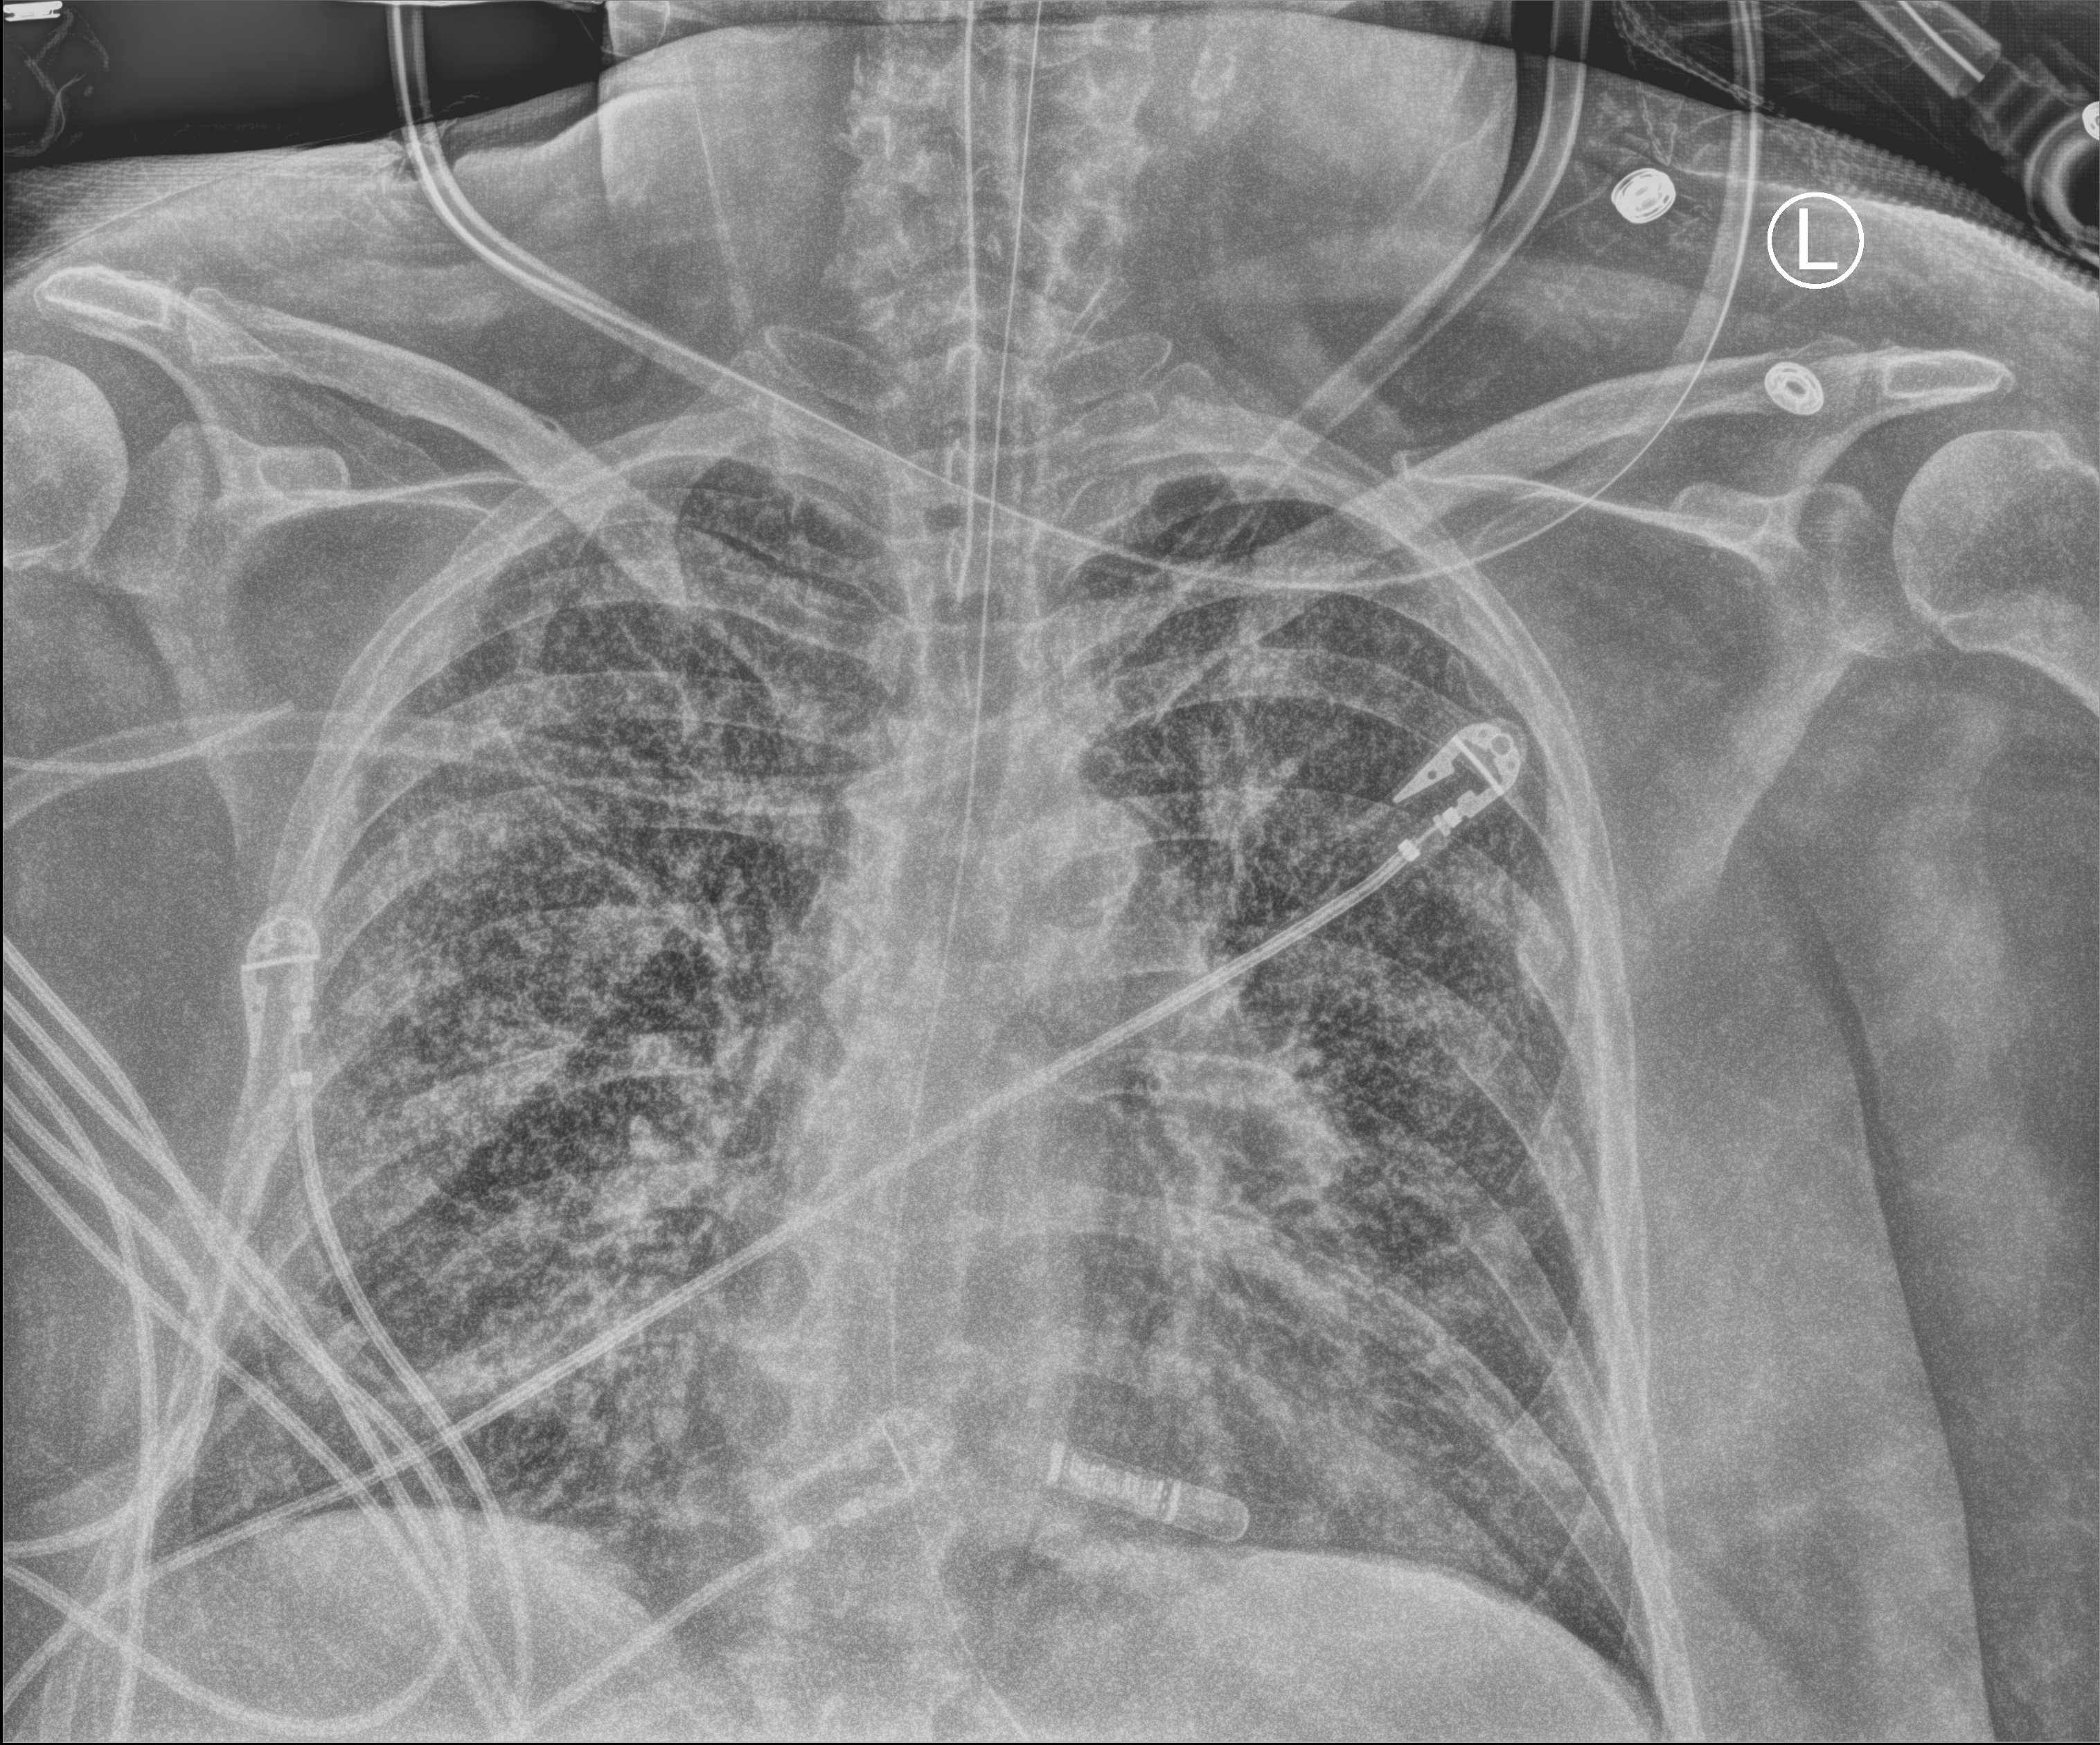
Chest X-ray (portable); anteroposterior (AP) projection. Patient hospitalised with COVID-19; female, aged 60–74 years.
From the hospital-stay record, not from the radiograph (when in the stay this image was taken is not recorded): admitted to intensive care during this hospital stay: yes; mechanically ventilated during this hospital stay: yes.